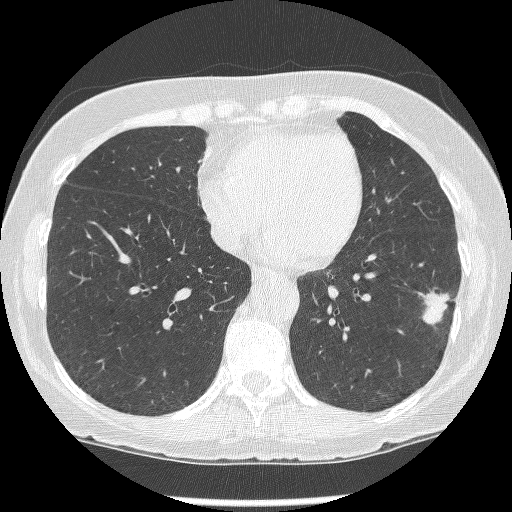
Axial slice from a low-dose chest CT screening exam, first (baseline) screen, lung window (W 1500 / L -600 HU), 1.25 mm slice thickness, slice 89 of 247 in the series. Female participant, aged 62 years at enrolment. Former smoker at enrolment.
Expert-annotated lung lesion, bounding box (x1, y1, x2, y2) in pixels: (420, 282, 462, 330). The screening reader recorded 2 non-calcified nodules or masses ≥4 mm on this exam; which of them this box marks is not recorded. Official screen result: positive, change unspecified: nodule(s) >= 4 mm or enlarging nodule(s), mass(es), or other non-specific abnormalities suspicious for lung cancer. Participant outcome: lung cancer diagnosed 15 days after this screen — non-small cell carcinoma, left lower lobe, stage IIIB (AJCC 6th edition), 23 mm at pathology.